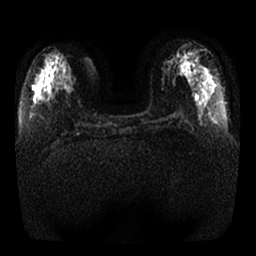
Breast MRI, one axial slice; slice 9 of 25 in the series (ordered by position); diffusion-weighted series; image 2 of 4 stored at this slice position (different b-values; order by instance number); 1.5 T; 4 mm slice thickness; 256 × 256 image matrix. Female patient.
Structures marked on this image (outlined manually by an expert reader):
- tumour on diffusion-weighted imaging: bounding box [x1, y1, x2, y2] px = [64, 83, 71, 91]